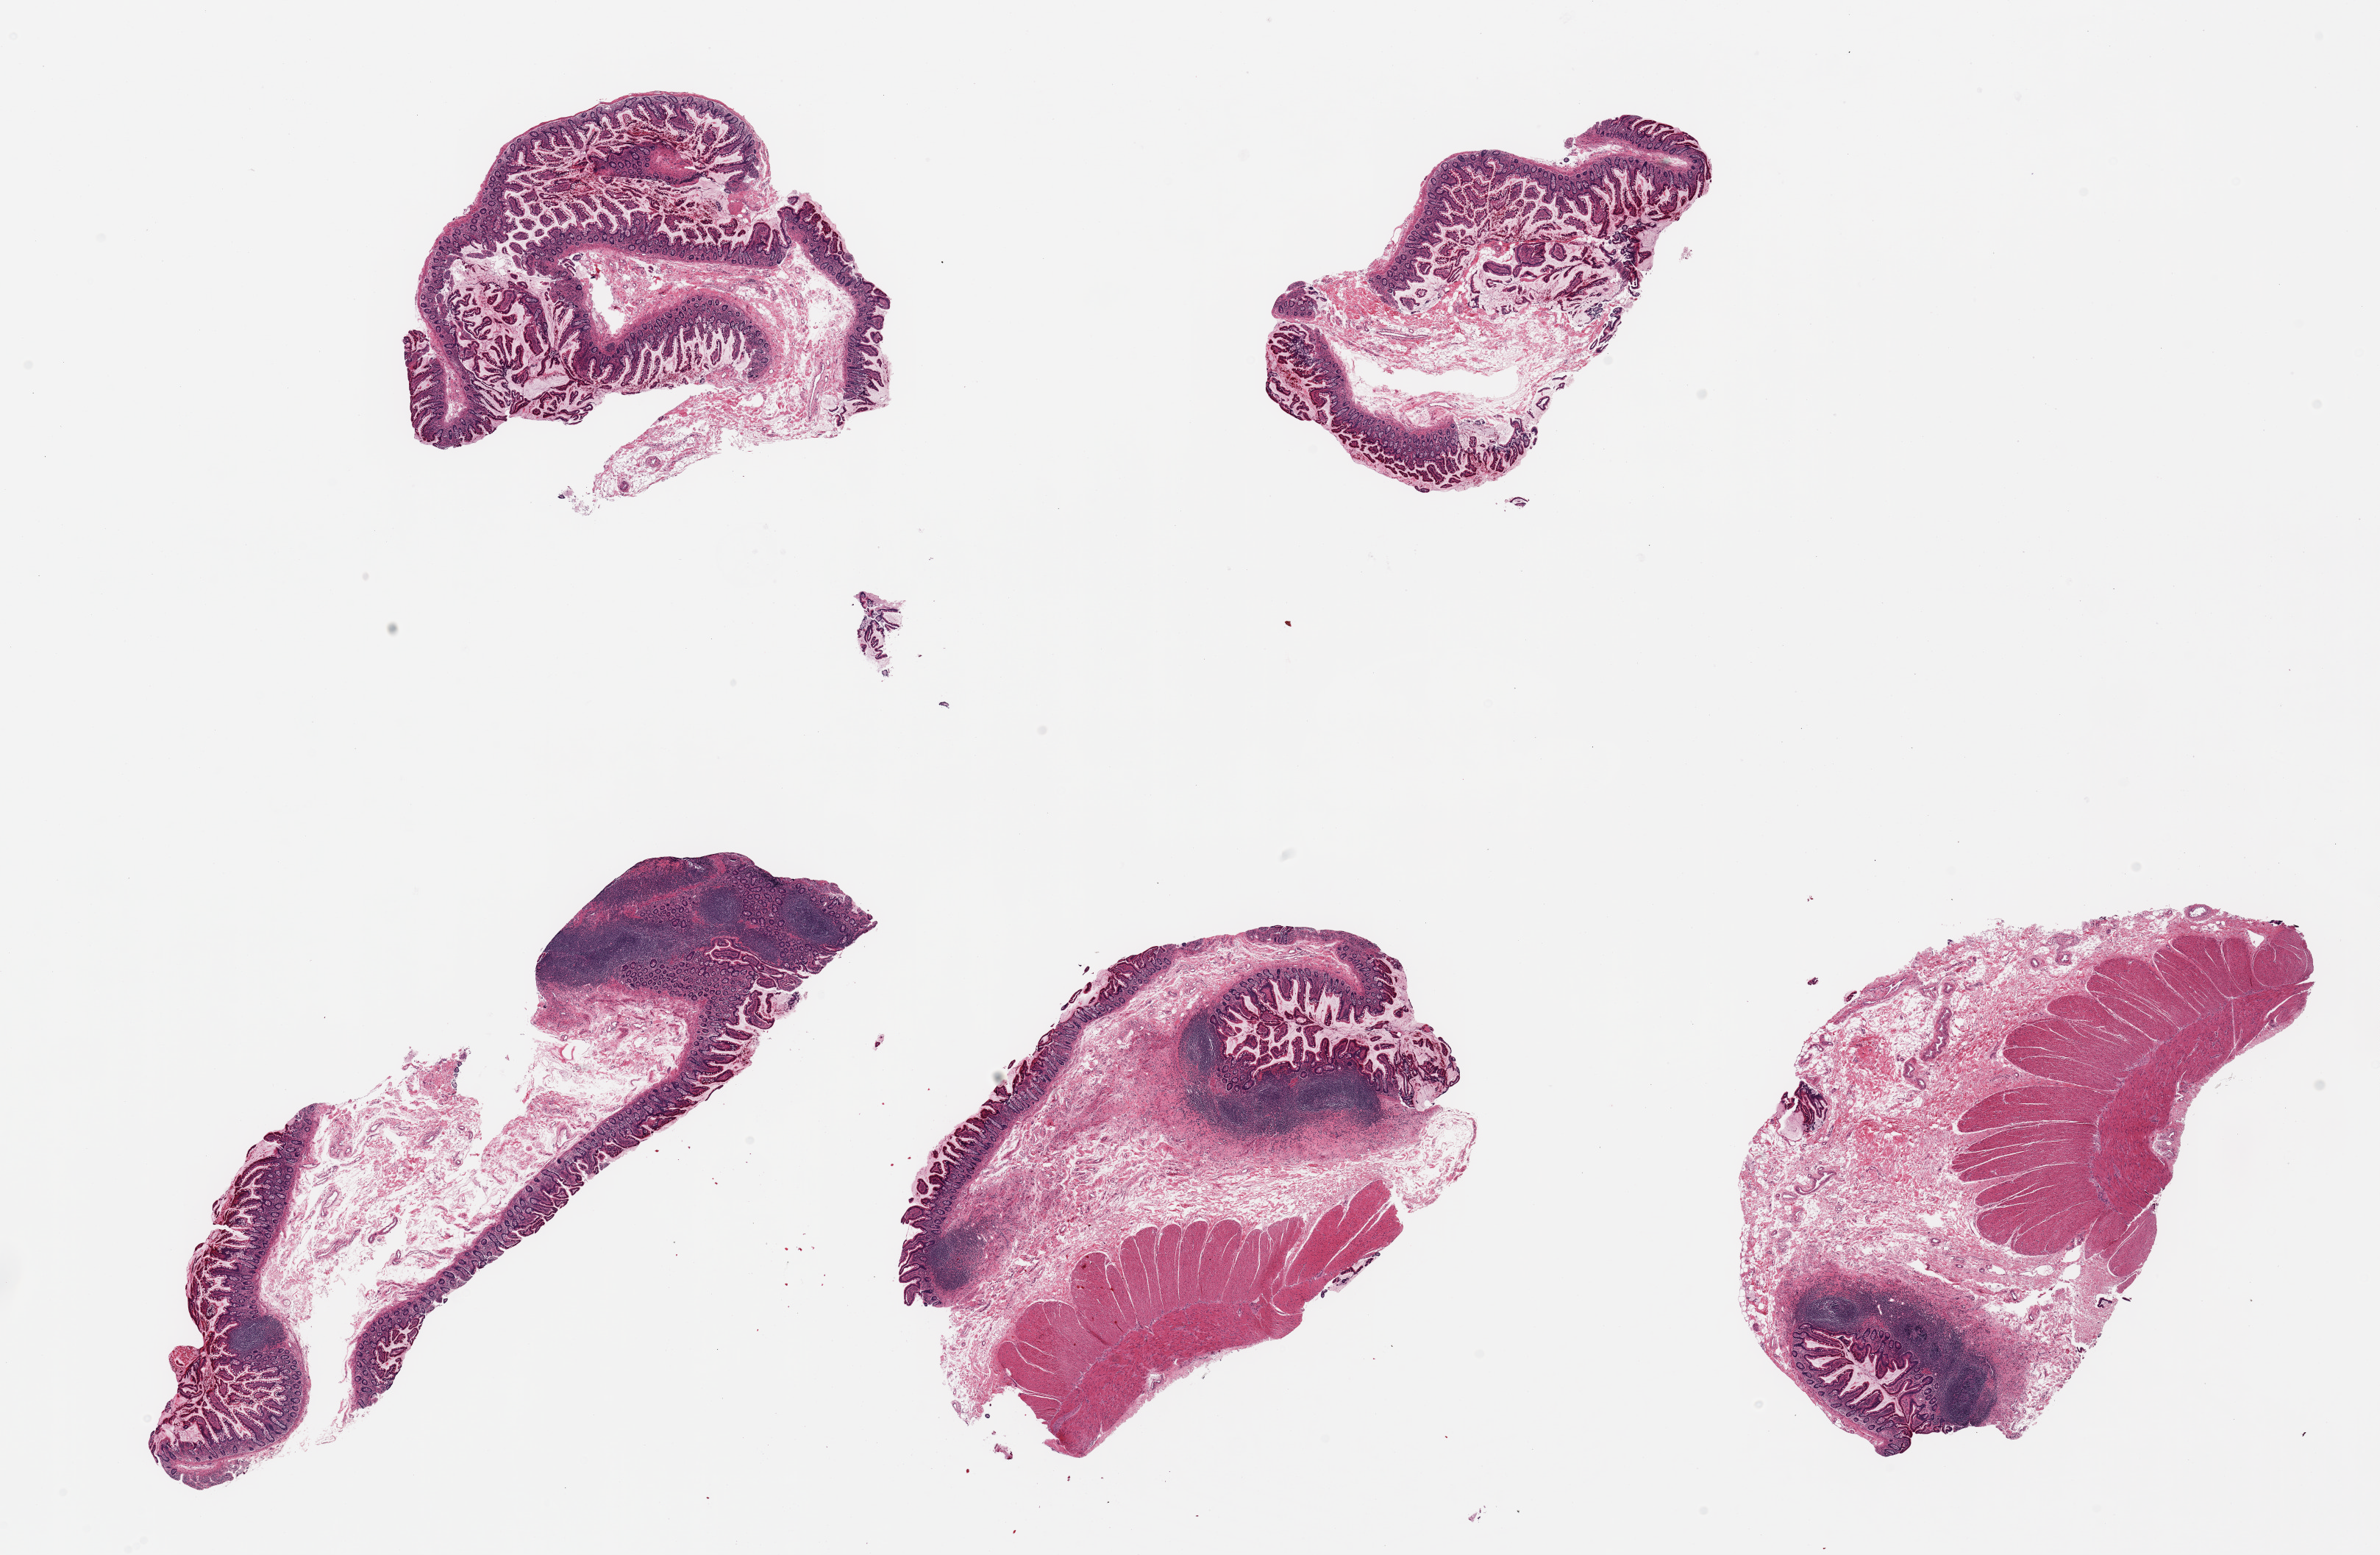
Whole-slide image, H&E stain, a low-resolution overview of the entire scanned area, about 25.6 x 16.7 mm (acquisition: 20x scan), PAXgene-fixed paraffin-embedded (PFPE) section, section of ileum (target tissue), donor tissue sample. Male donor.
* reviewer comment on this tissue sample: 5 pieces; lymphoid tissue in 3 pieces; muscle (non-target) present on 2 pieces